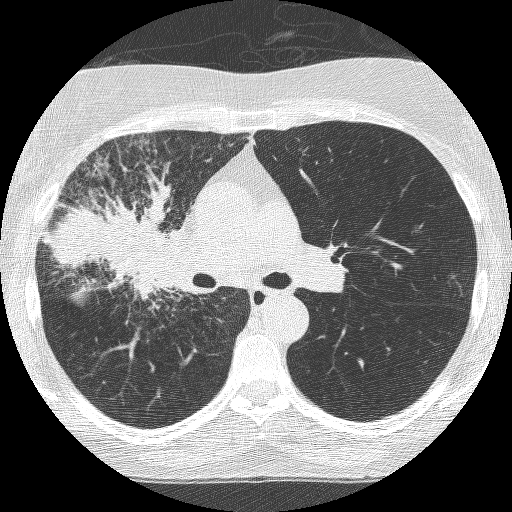
Axial slice from a low-dose chest CT screening exam, third annual screen, lung window (W 1500 / L -600 HU), 1.25 mm slice thickness, lung (sharp) reconstruction kernel (BONE), 120 kVp, slice 158 of 253 in the series, 512 × 512 image matrix. Female, age 64 years at enrolment. Former smoker at enrolment.
Expert reader's lesion annotation, bounding box [x1, y1, x2, y2] px = [76, 197, 203, 325]. Reader record for this screening exam (exam-level; its link to the box is not recorded): non-calcified nodule or mass ≥4 mm, right upper lobe, 49 × 43 mm, spiculated (stellate) margins, soft tissue attenuation, pre-existing on the prior screen: yes; interval growth: yes.